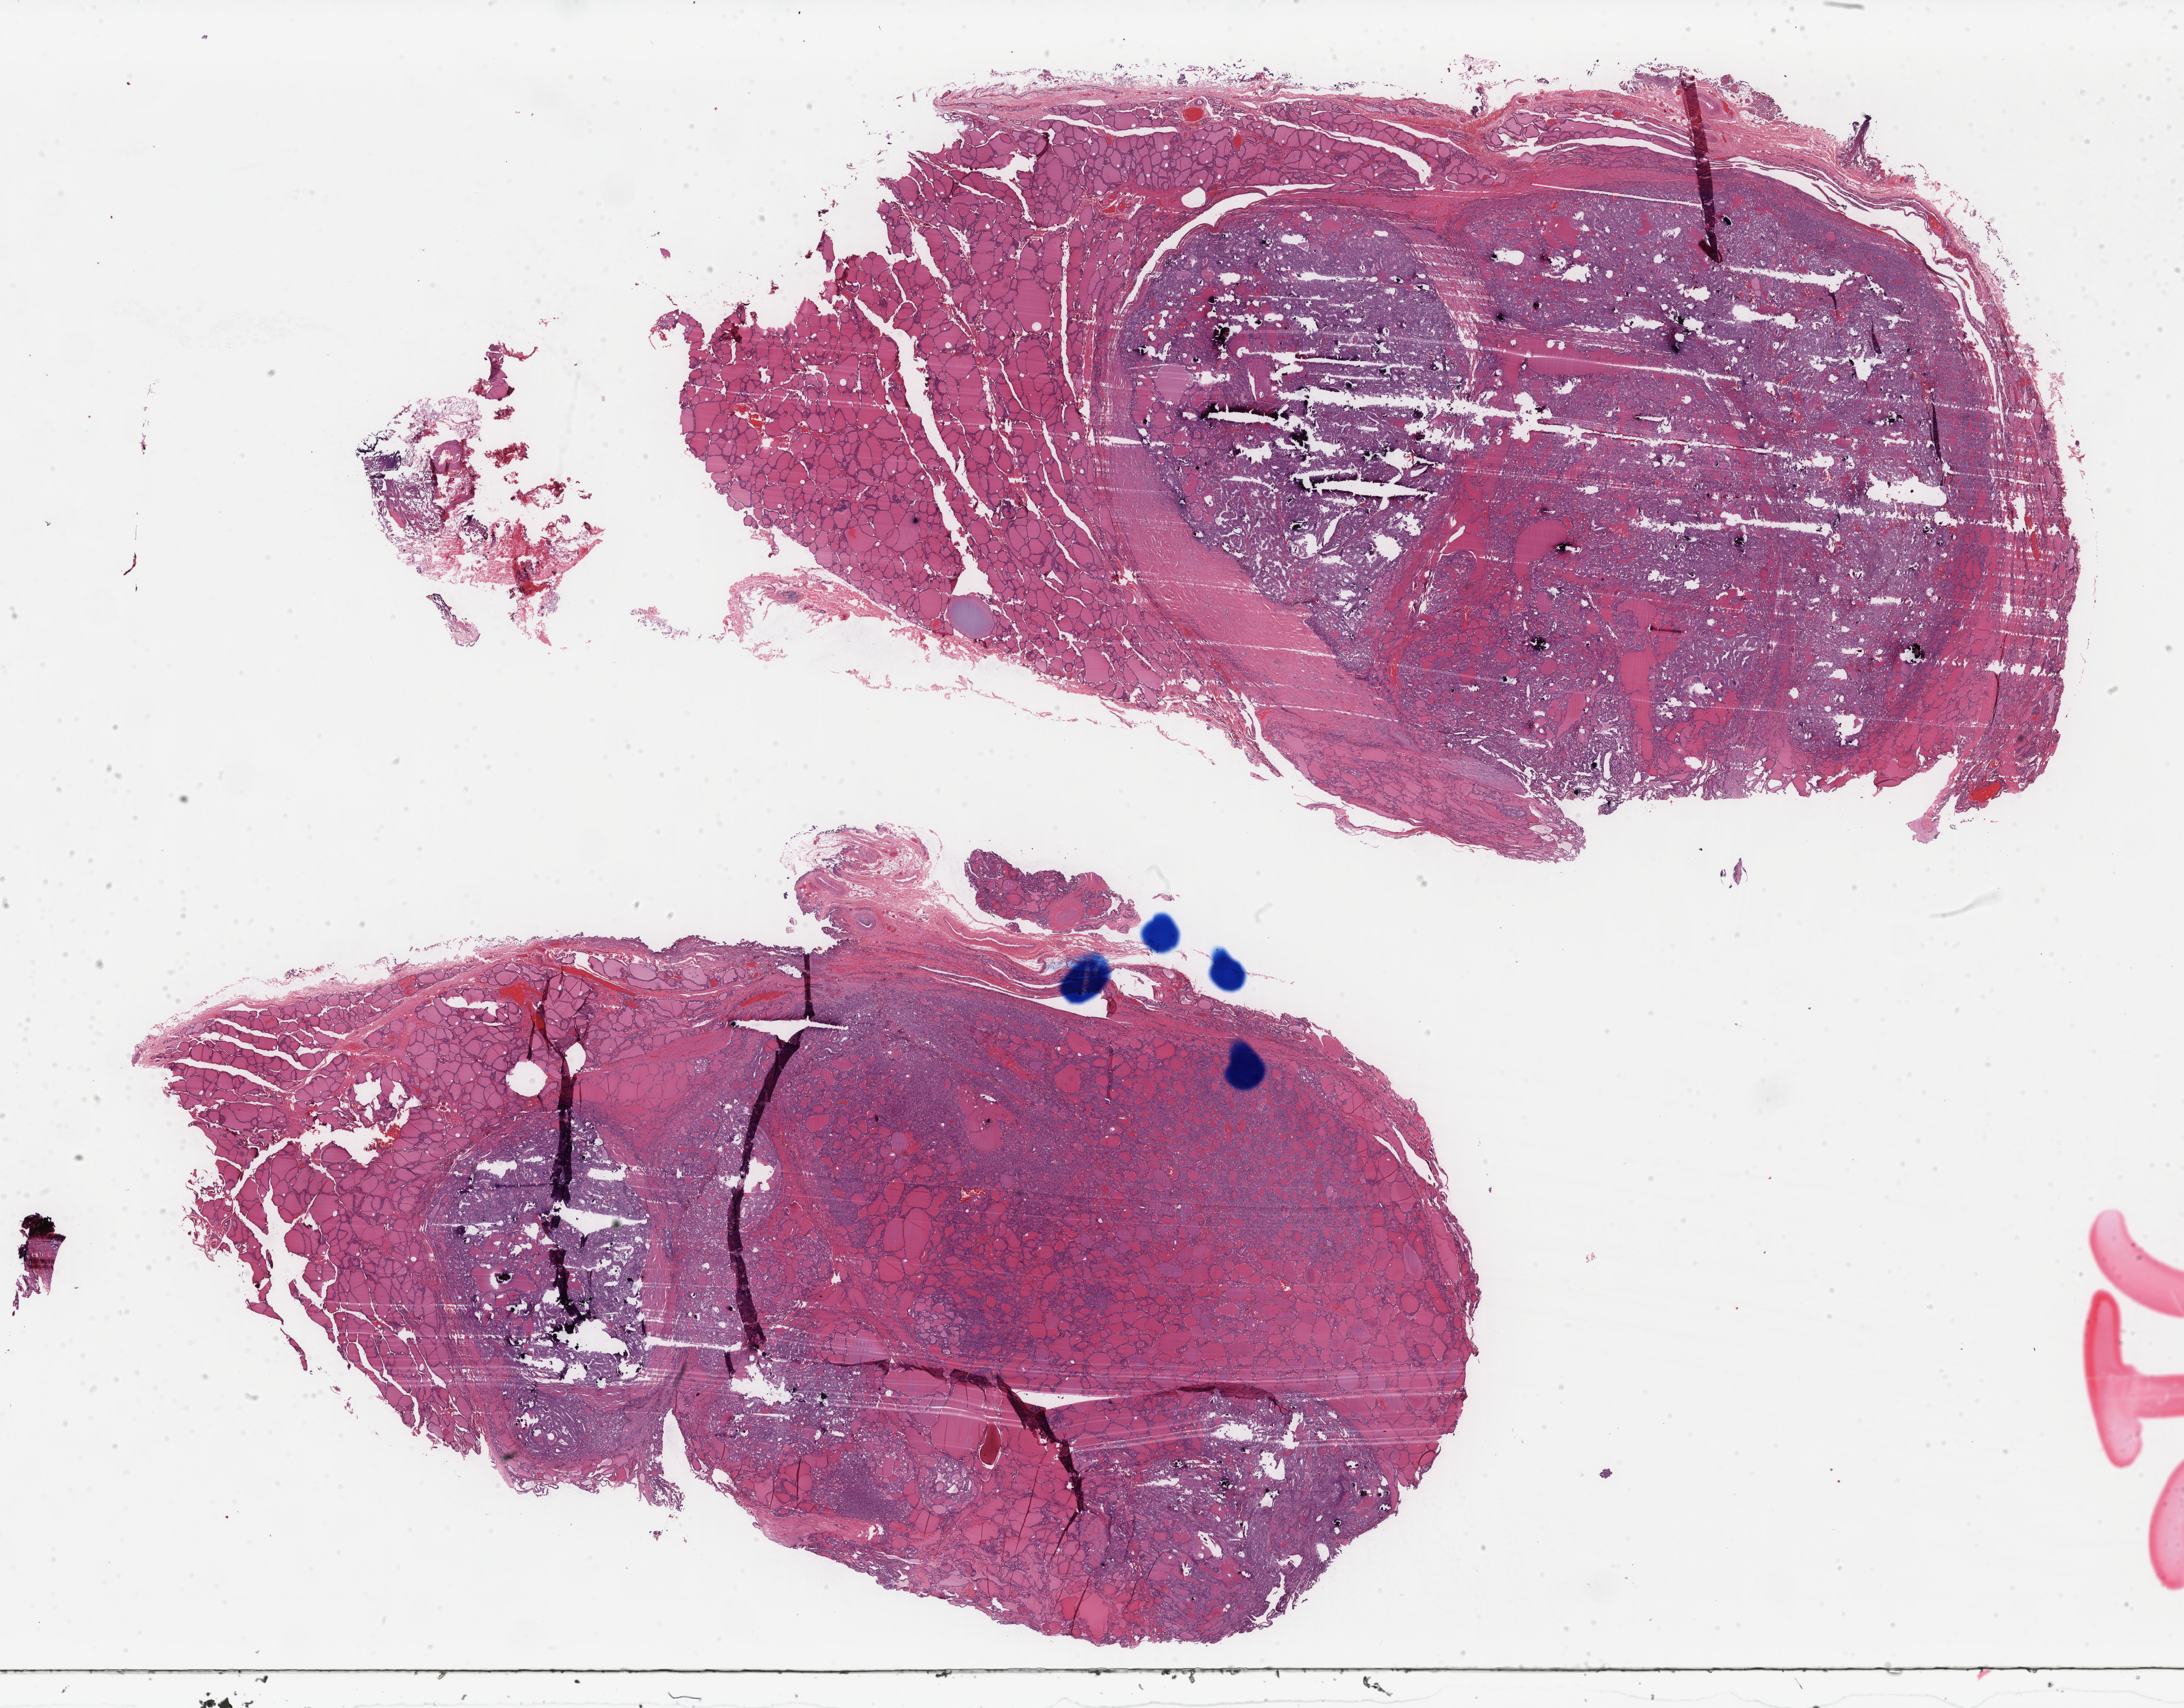
Digitized H&E tissue section (whole slide), whole scanned area (about 29.5 x 23.1 mm, from a 40x scan) shown as a low-resolution overview. FFPE section. Thyroid, primary tumour sample. Patient: female, age at initial diagnosis 30 years.
AJCC pathologic stage: I (7th edition). Diagnosis: Papillary adenocarcinoma, NOS. TNM: T1b N0 M0. Laterality: right.